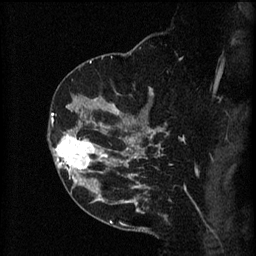
Breast MRI (dynamic contrast-enhanced), one sagittal slice. Position 38 of 60 along the scan axis. 3 images stored at this slice position (order not interpretable as contrast timing). 1.5 T. TE 4.2 ms, TR 8.2 ms. 2 mm slice thickness. 256 × 256 image matrix, field of view 180 × 180 mm. Female patient, age 49 years.
Structures marked on this image (semi-automatically segmented with operator editing):
- analysis volume of interest (the breast-tissue region the enhancement analysis was run in; not a lesion): bounding box [x1, y1, x2, y2] px = [48, 126, 105, 177]
- tumour enhancement mask (voxels above the 70 % enhancement threshold inside the analysis volume of interest): [53, 134, 105, 177]